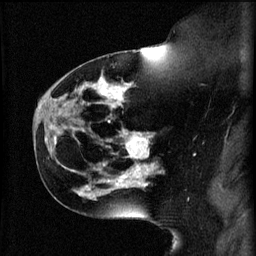
Breast MRI (dynamic contrast-enhanced), one sagittal slice; slice 37 of 60 in the series (ordered by position); 3 images stored at this slice position (order not interpretable as contrast timing); 1.5 T; TE 4.2 ms, TR 11 ms; 2 mm slice thickness; 256 × 256 image matrix. Patient: female, 44 years.
Annotated regions visible in this slice (semi-automatic segmentation, software-assisted and operator-edited):
- analysis volume of interest (the breast-tissue region the enhancement analysis was run in; not a lesion): bounding box <110,130,159,179> (left, top, right, bottom; pixels)
- tumour enhancement mask (voxels above the 70 % enhancement threshold inside the analysis volume of interest): <118,130,157,179>